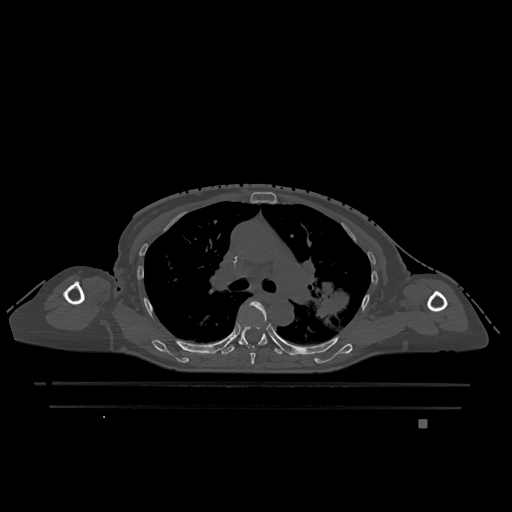
CT including the spine, one axial slice; position 810 of 1317 along the scan axis; bone window (W 1800 / L 400 HU); 0.5 mm slice thickness; 512 × 512 image matrix. Female patient, age 74 years. Case-level facts recorded for this patient, not image findings: primary cancer: lung.
Structures marked on this image (semi-automatically segmented with operator editing):
- T5 vertebra: box from (x=243, y=301) to (x=267, y=364) px
- T6 vertebra: (x=222, y=325)–(x=282, y=355)